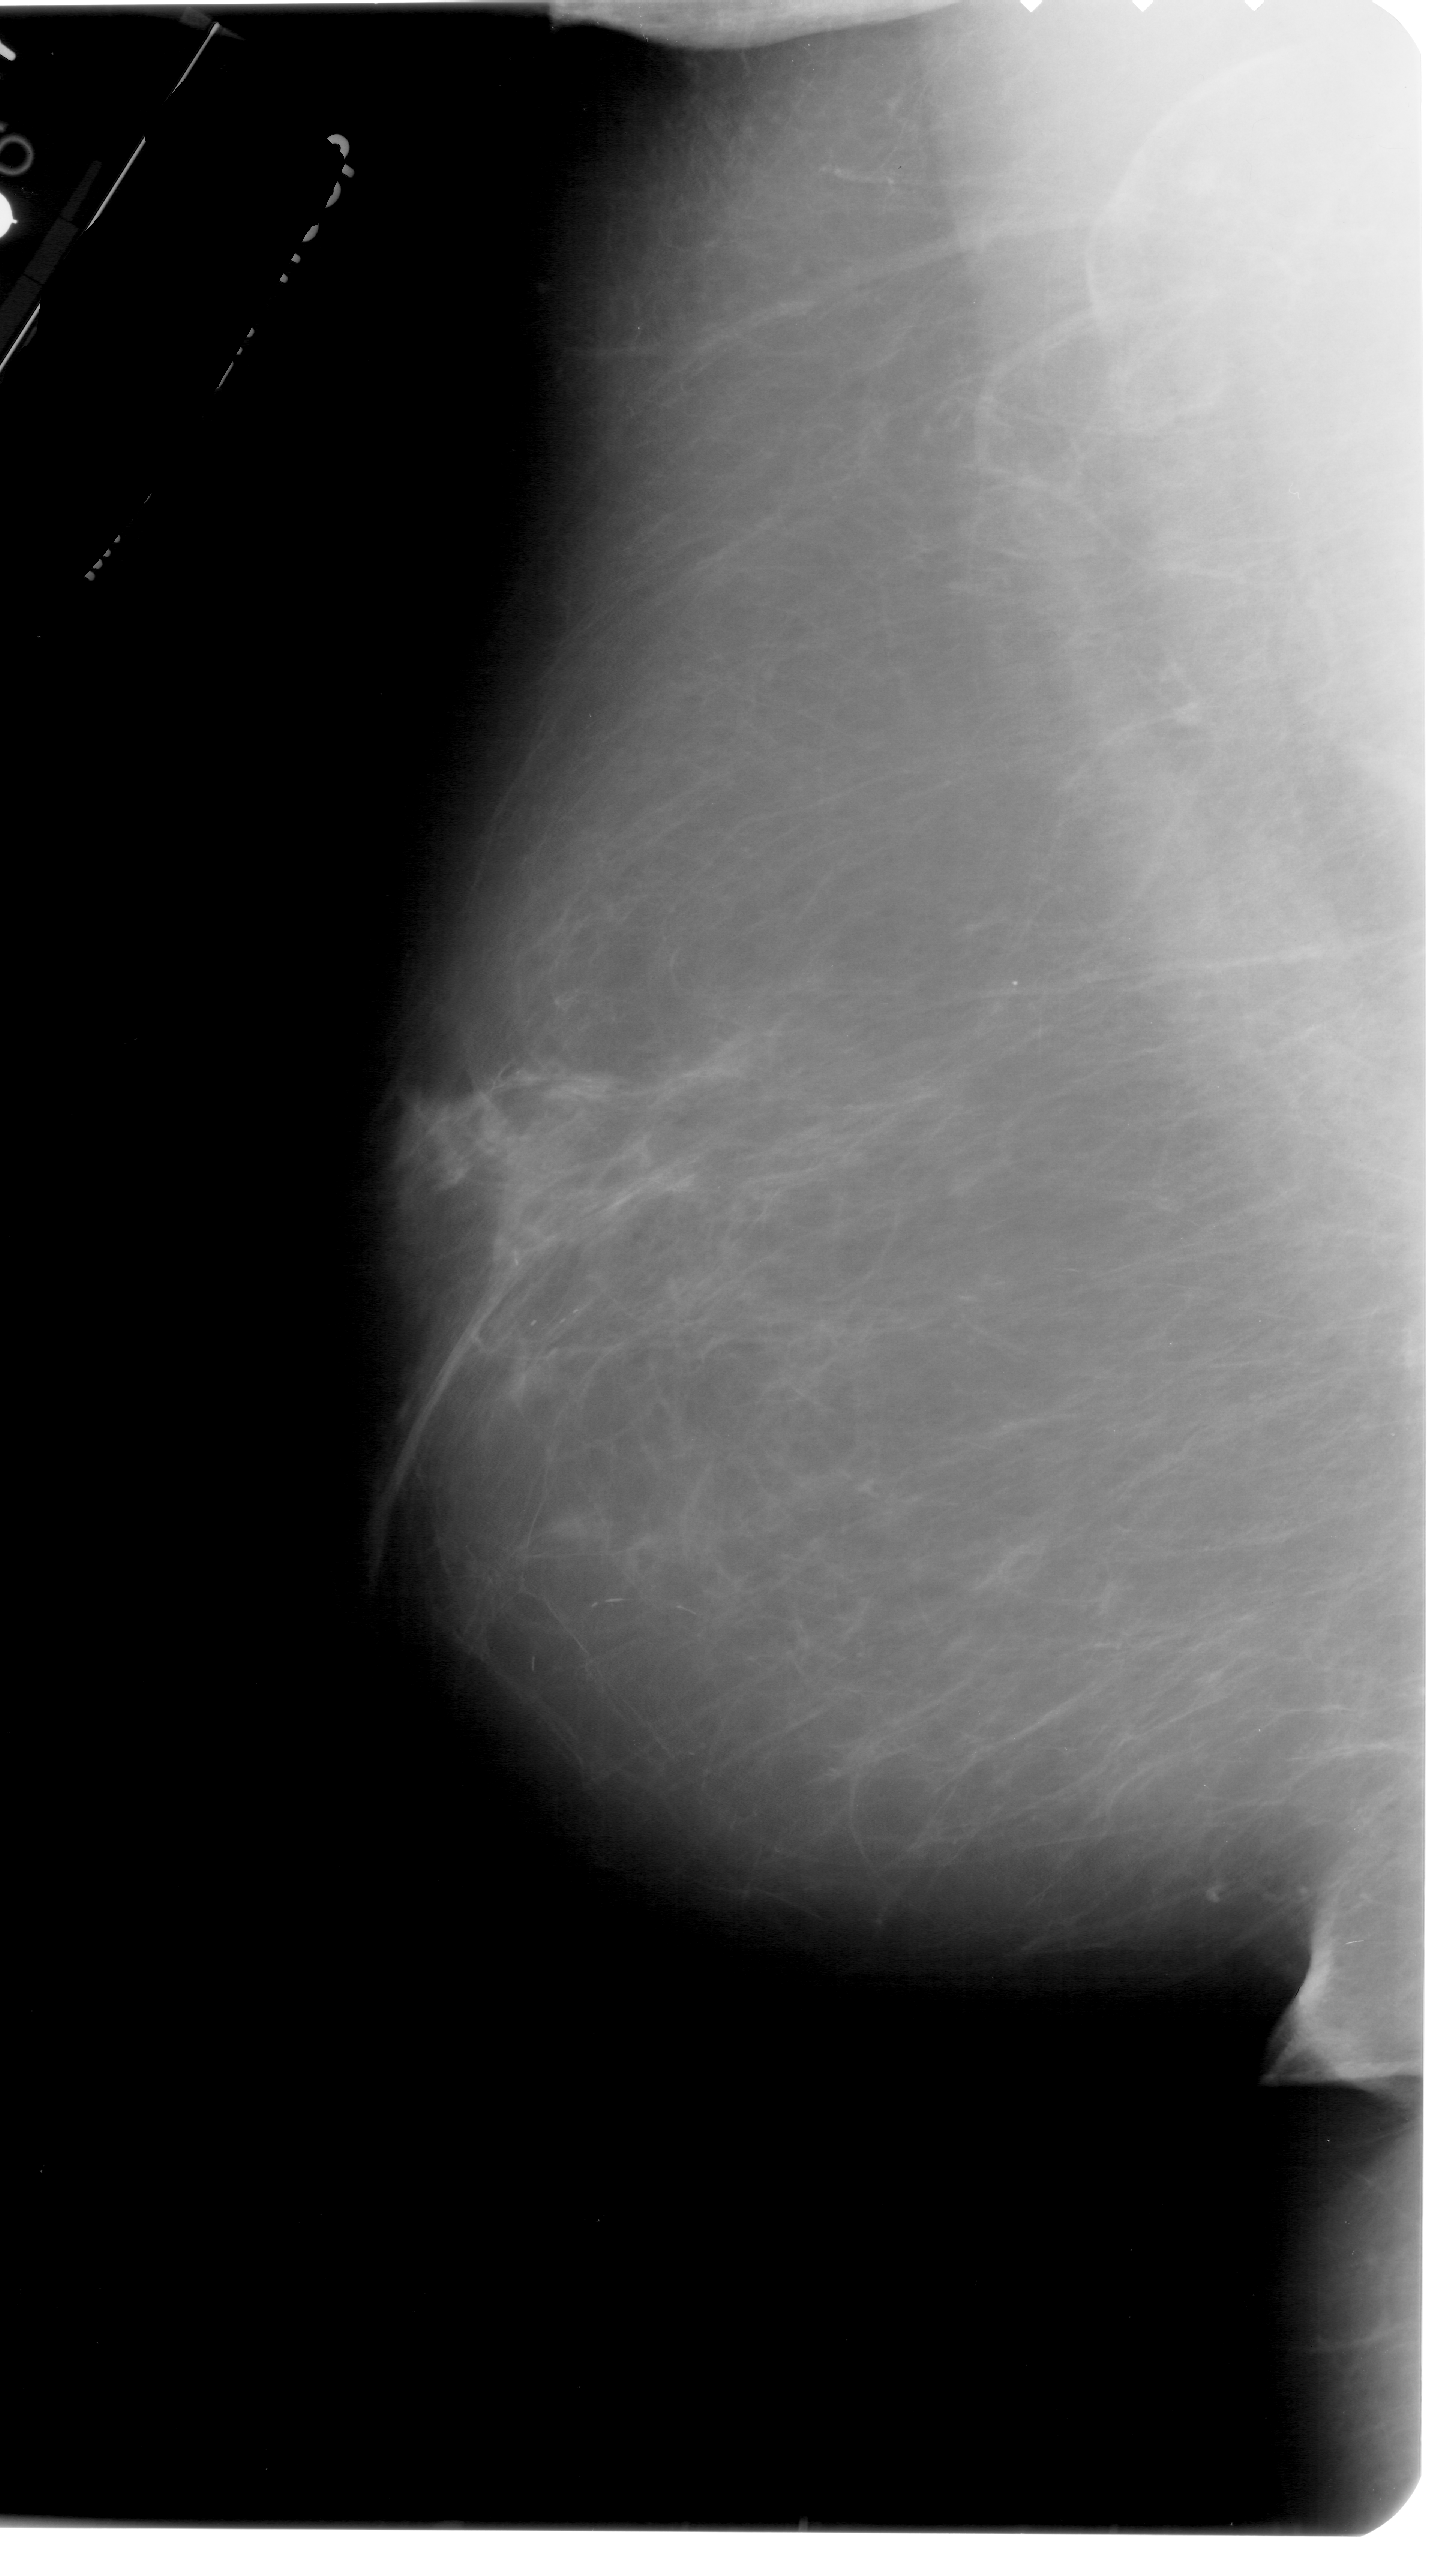
Mammogram (digitized film); left breast; MLO view; breast composition: scattered fibroglandular densities (BI-RADS density category 2 of 4).
Calcifications, morphology pleomorphic, distribution clustered; BI-RADS assessment category 4; subtlety rating 2 on a 1 (subtle) to 5 (obvious) scale; pathology result (as recorded, not read from the image): malignant.